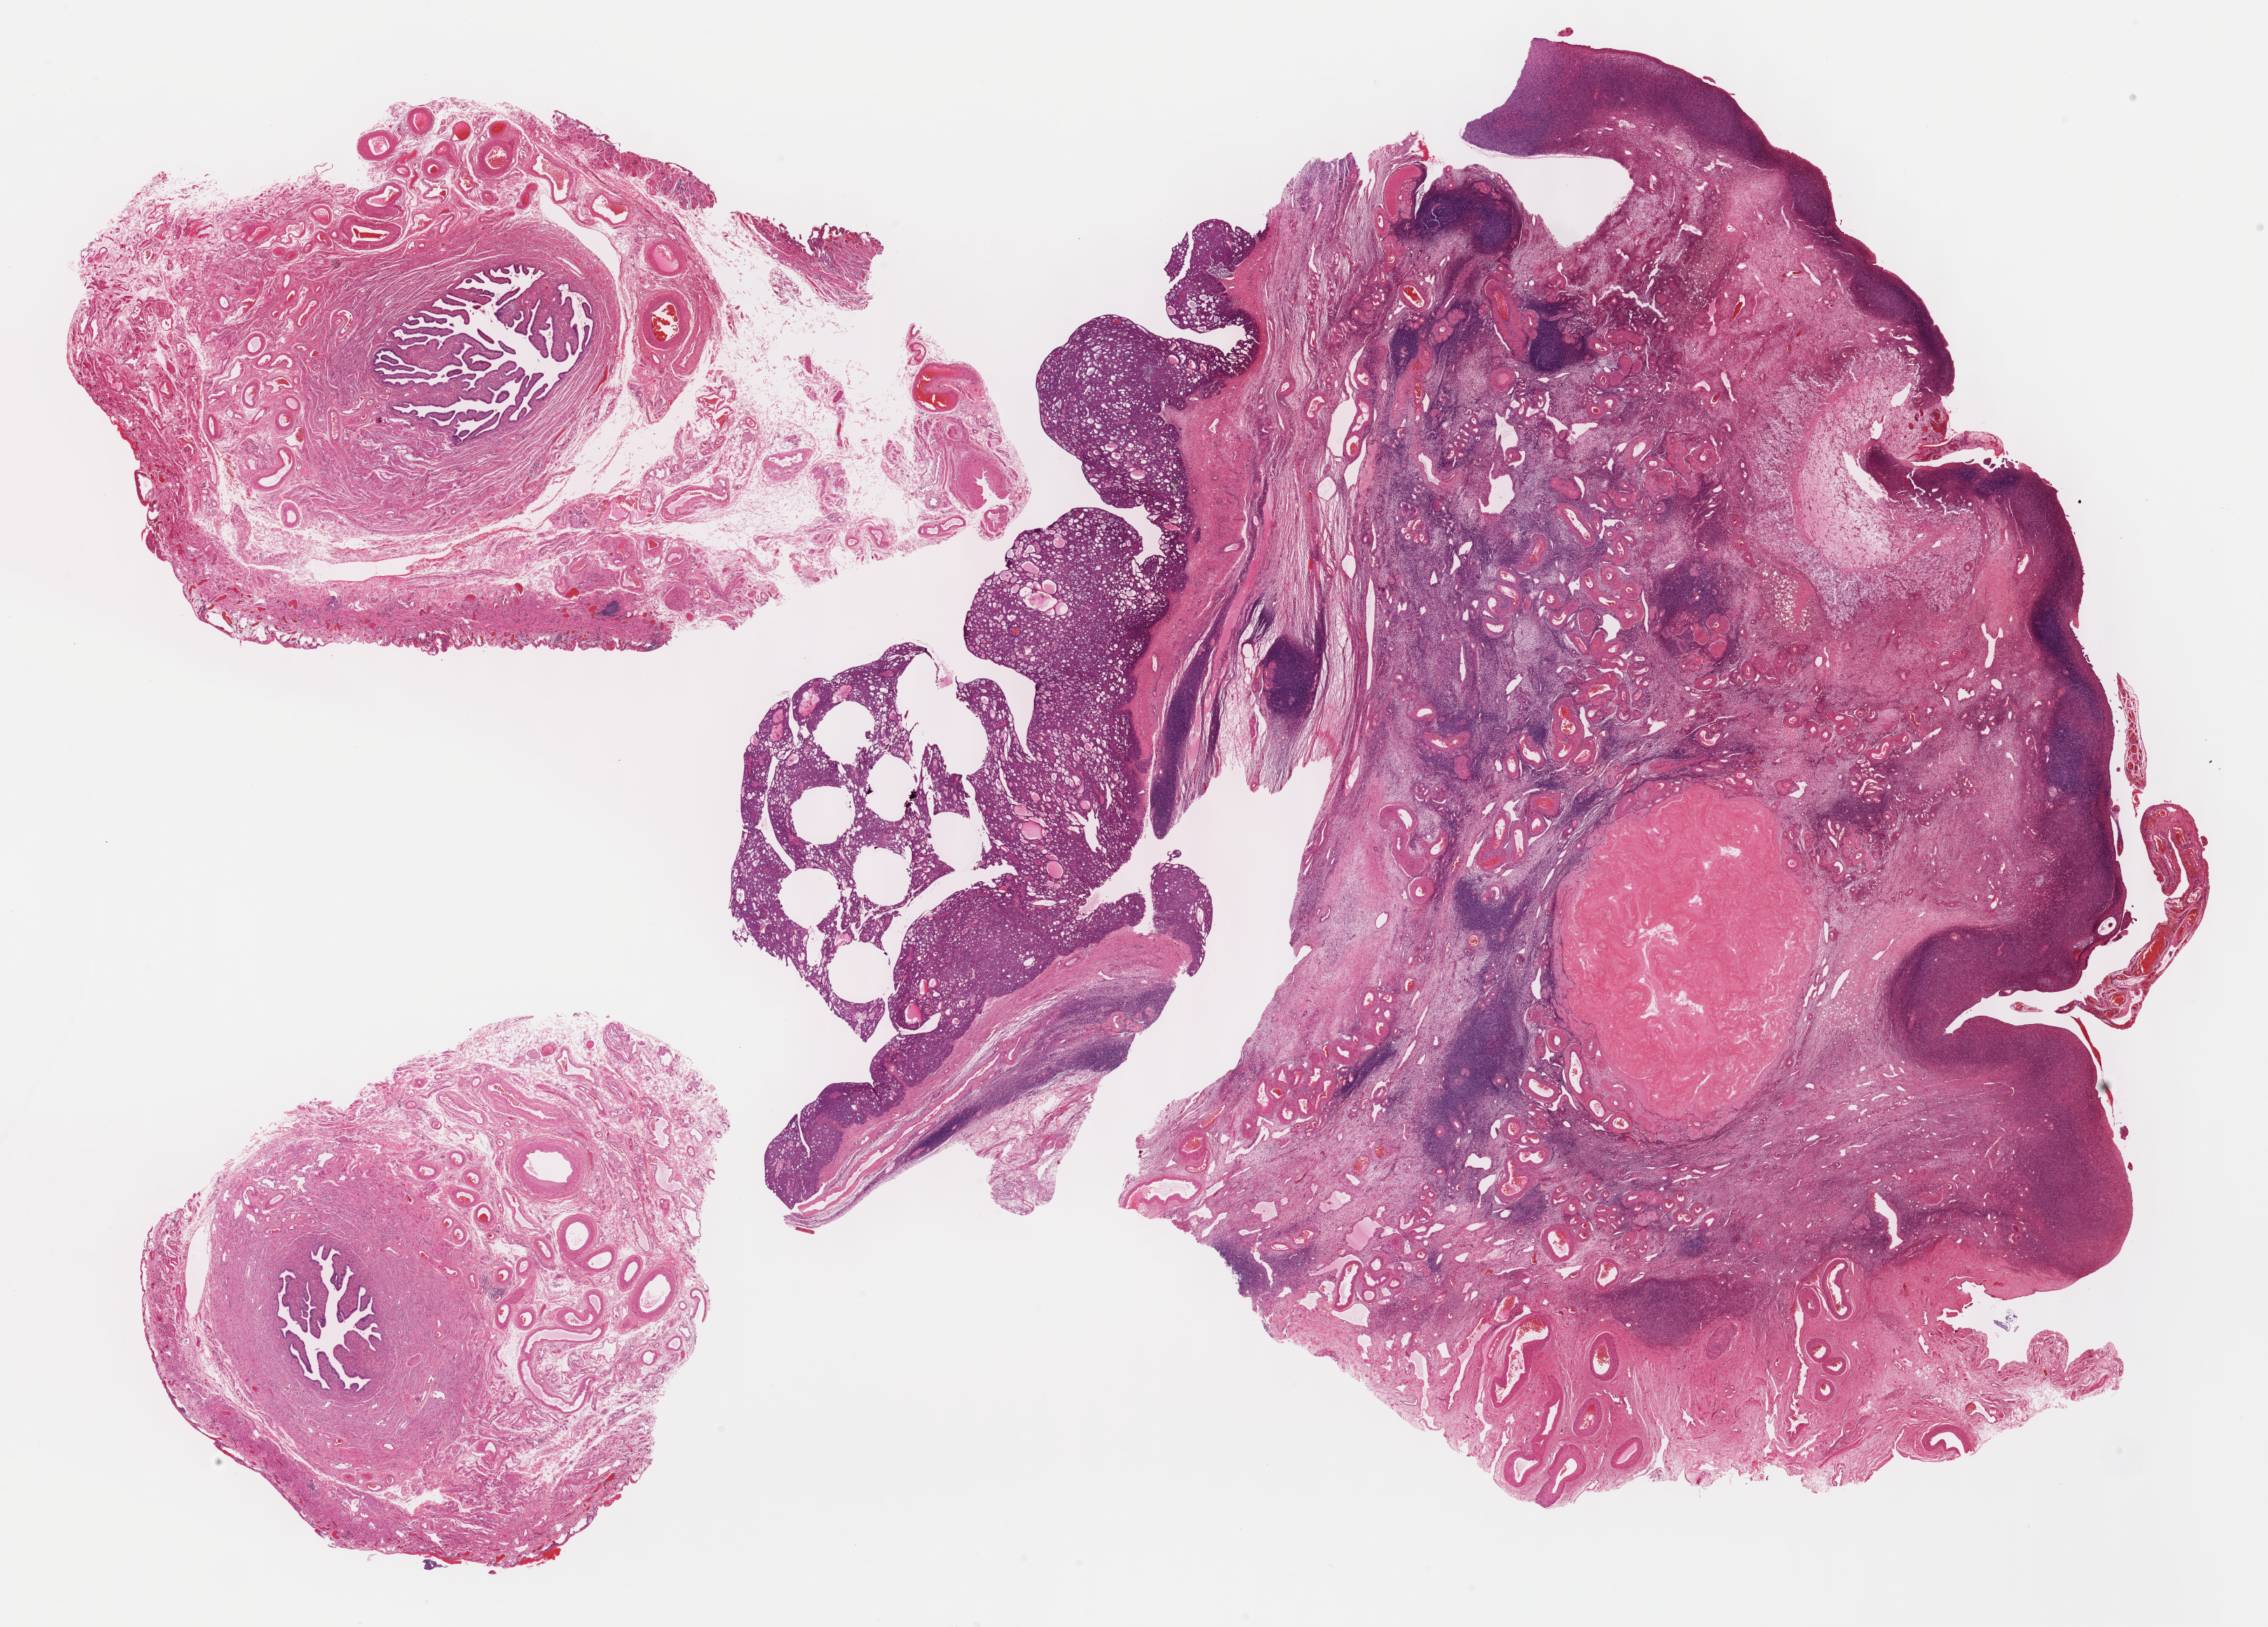
Digitized H&E tissue section (whole slide) — a low-resolution overview of the entire scanned area, about 26.2 x 18.8 mm (acquisition: 40x scan). Formalin-fixed paraffin-embedded (FFPE) diagnostic section. Sample: primary tumour, ovary. Female, age 45 years at initial diagnosis. Histologic grade: G3 (poorly differentiated).
* pathologic diagnosis: Serous cystadenocarcinoma, NOS
* FIGO stage: IIIC
* laterality: left